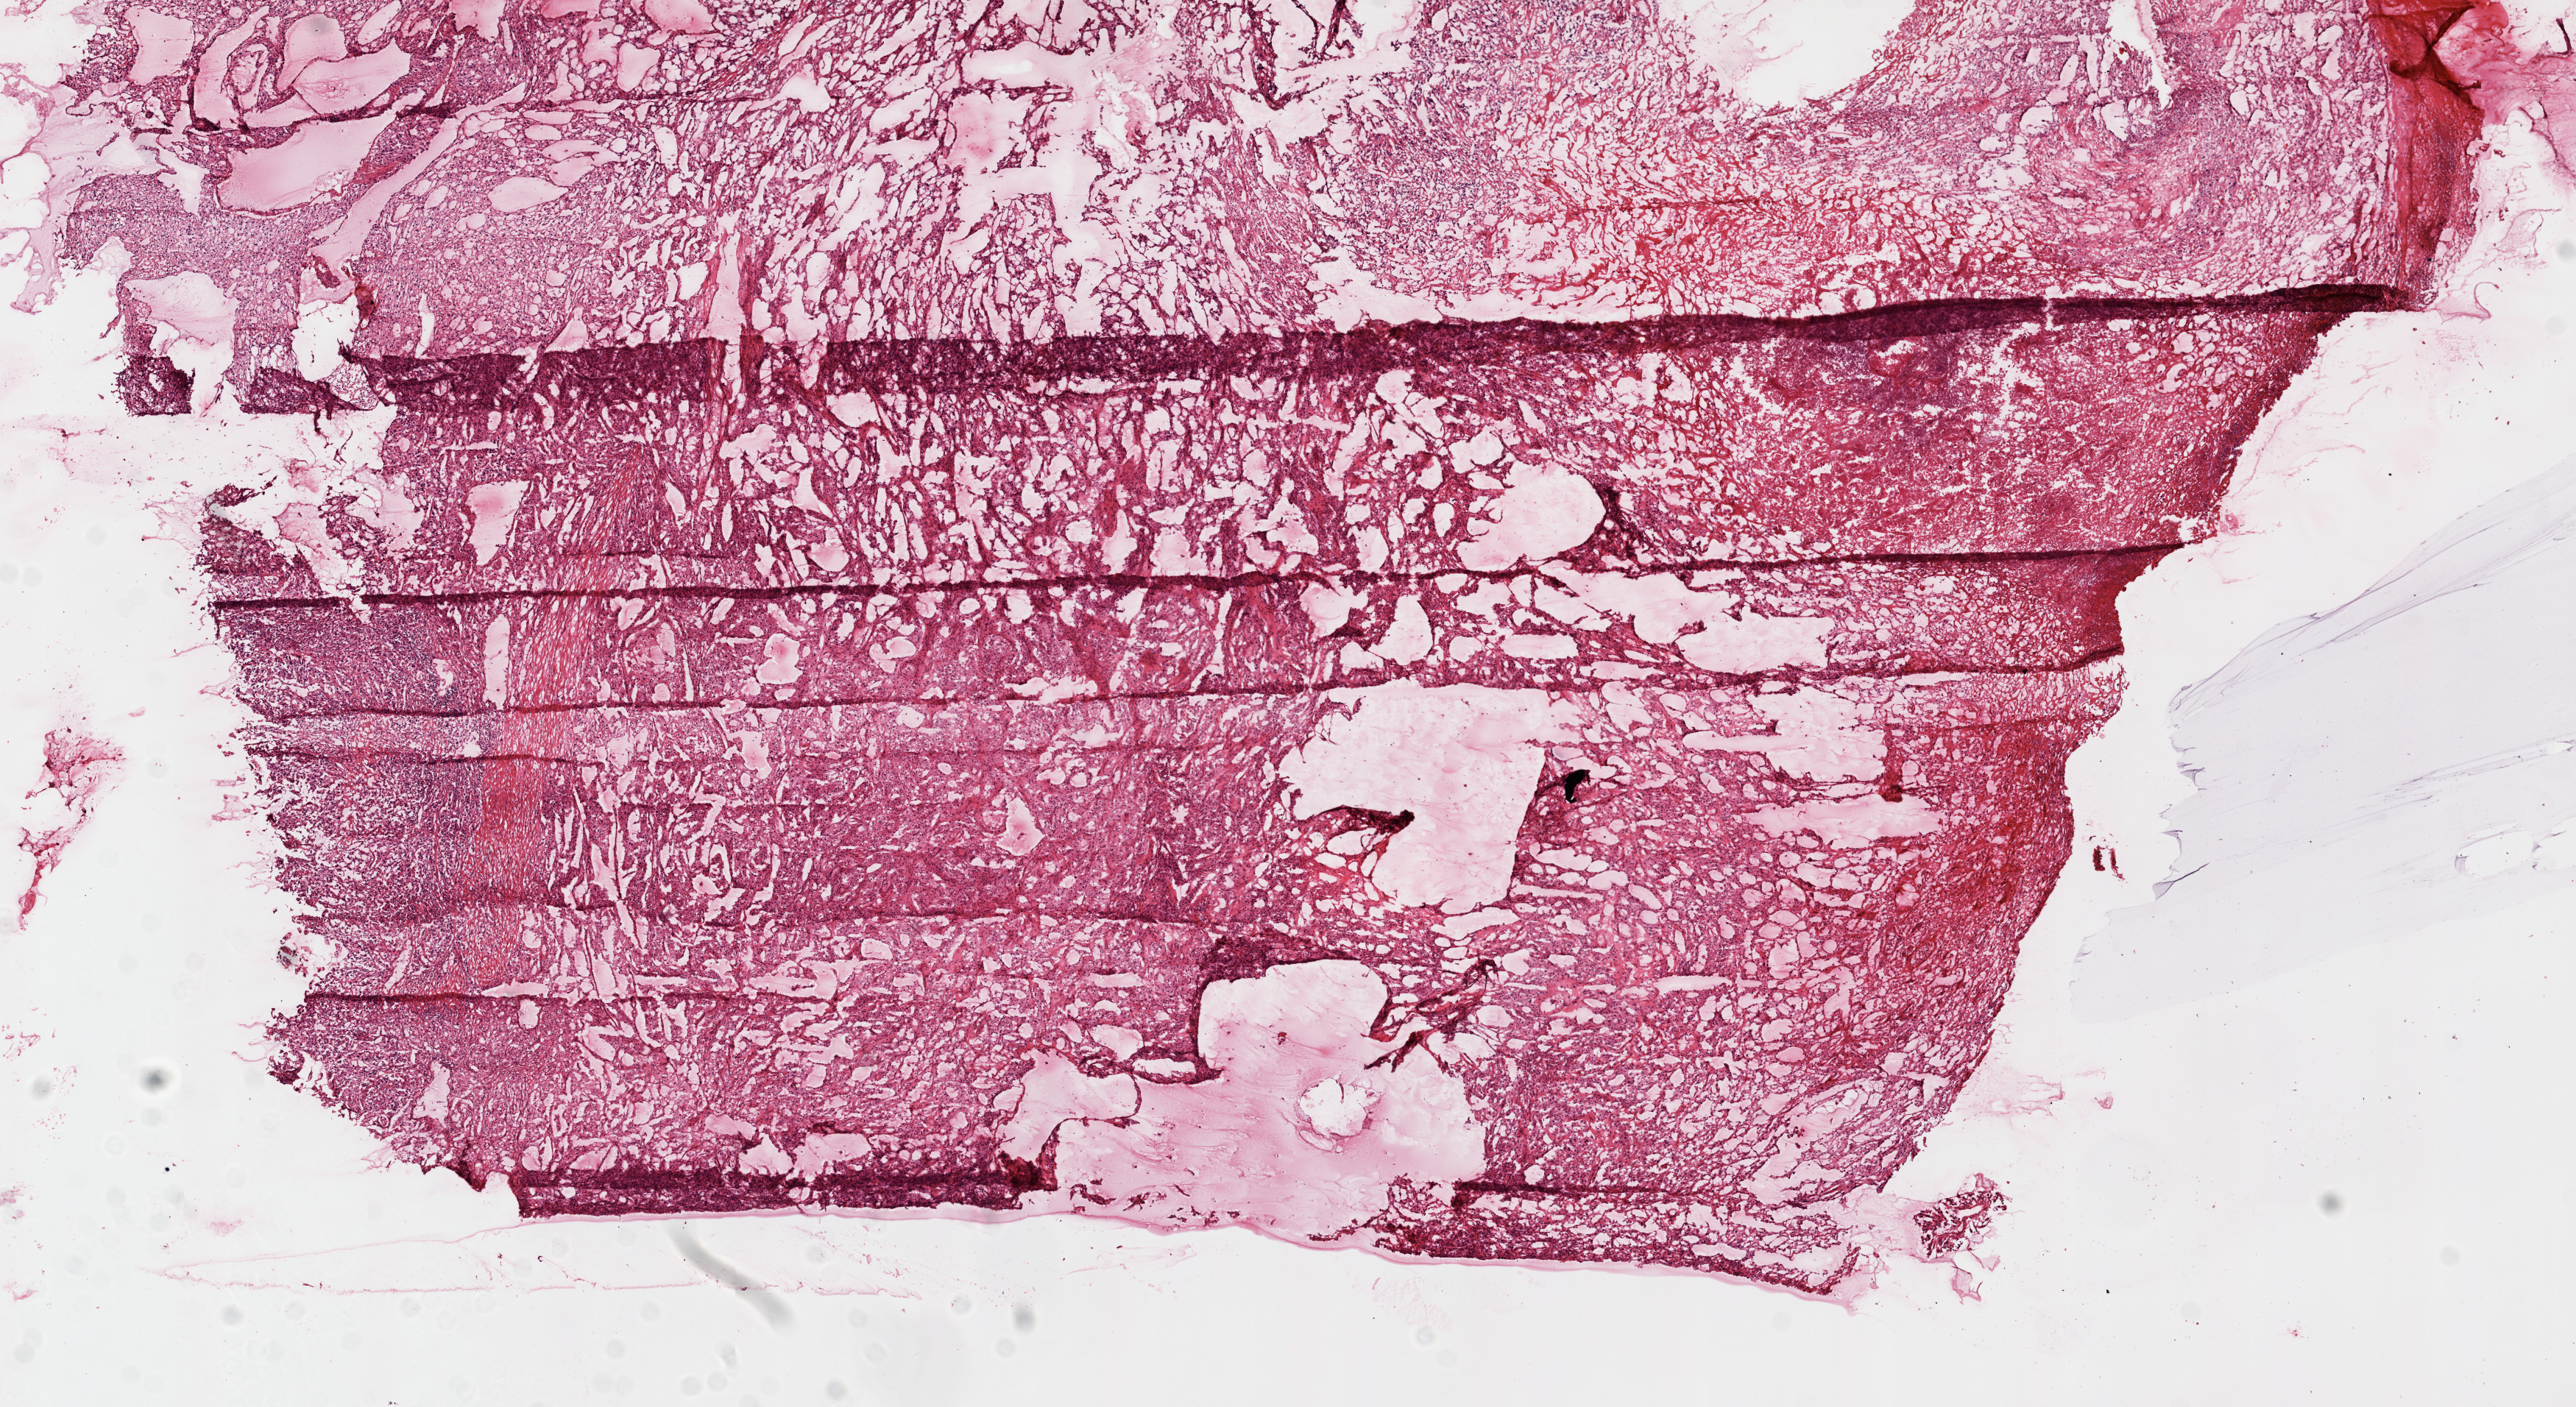
Digitized H&E tissue section (whole slide) — whole scanned area (about 14.0 x 7.7 mm, slide scanned at 20x) shown as a low-resolution overview, frozen section from the top of the tissue portion, sample: primary tumour, kidney. Female, age 68 years at initial diagnosis.
Histologic diagnosis: Clear cell adenocarcinoma, NOS.